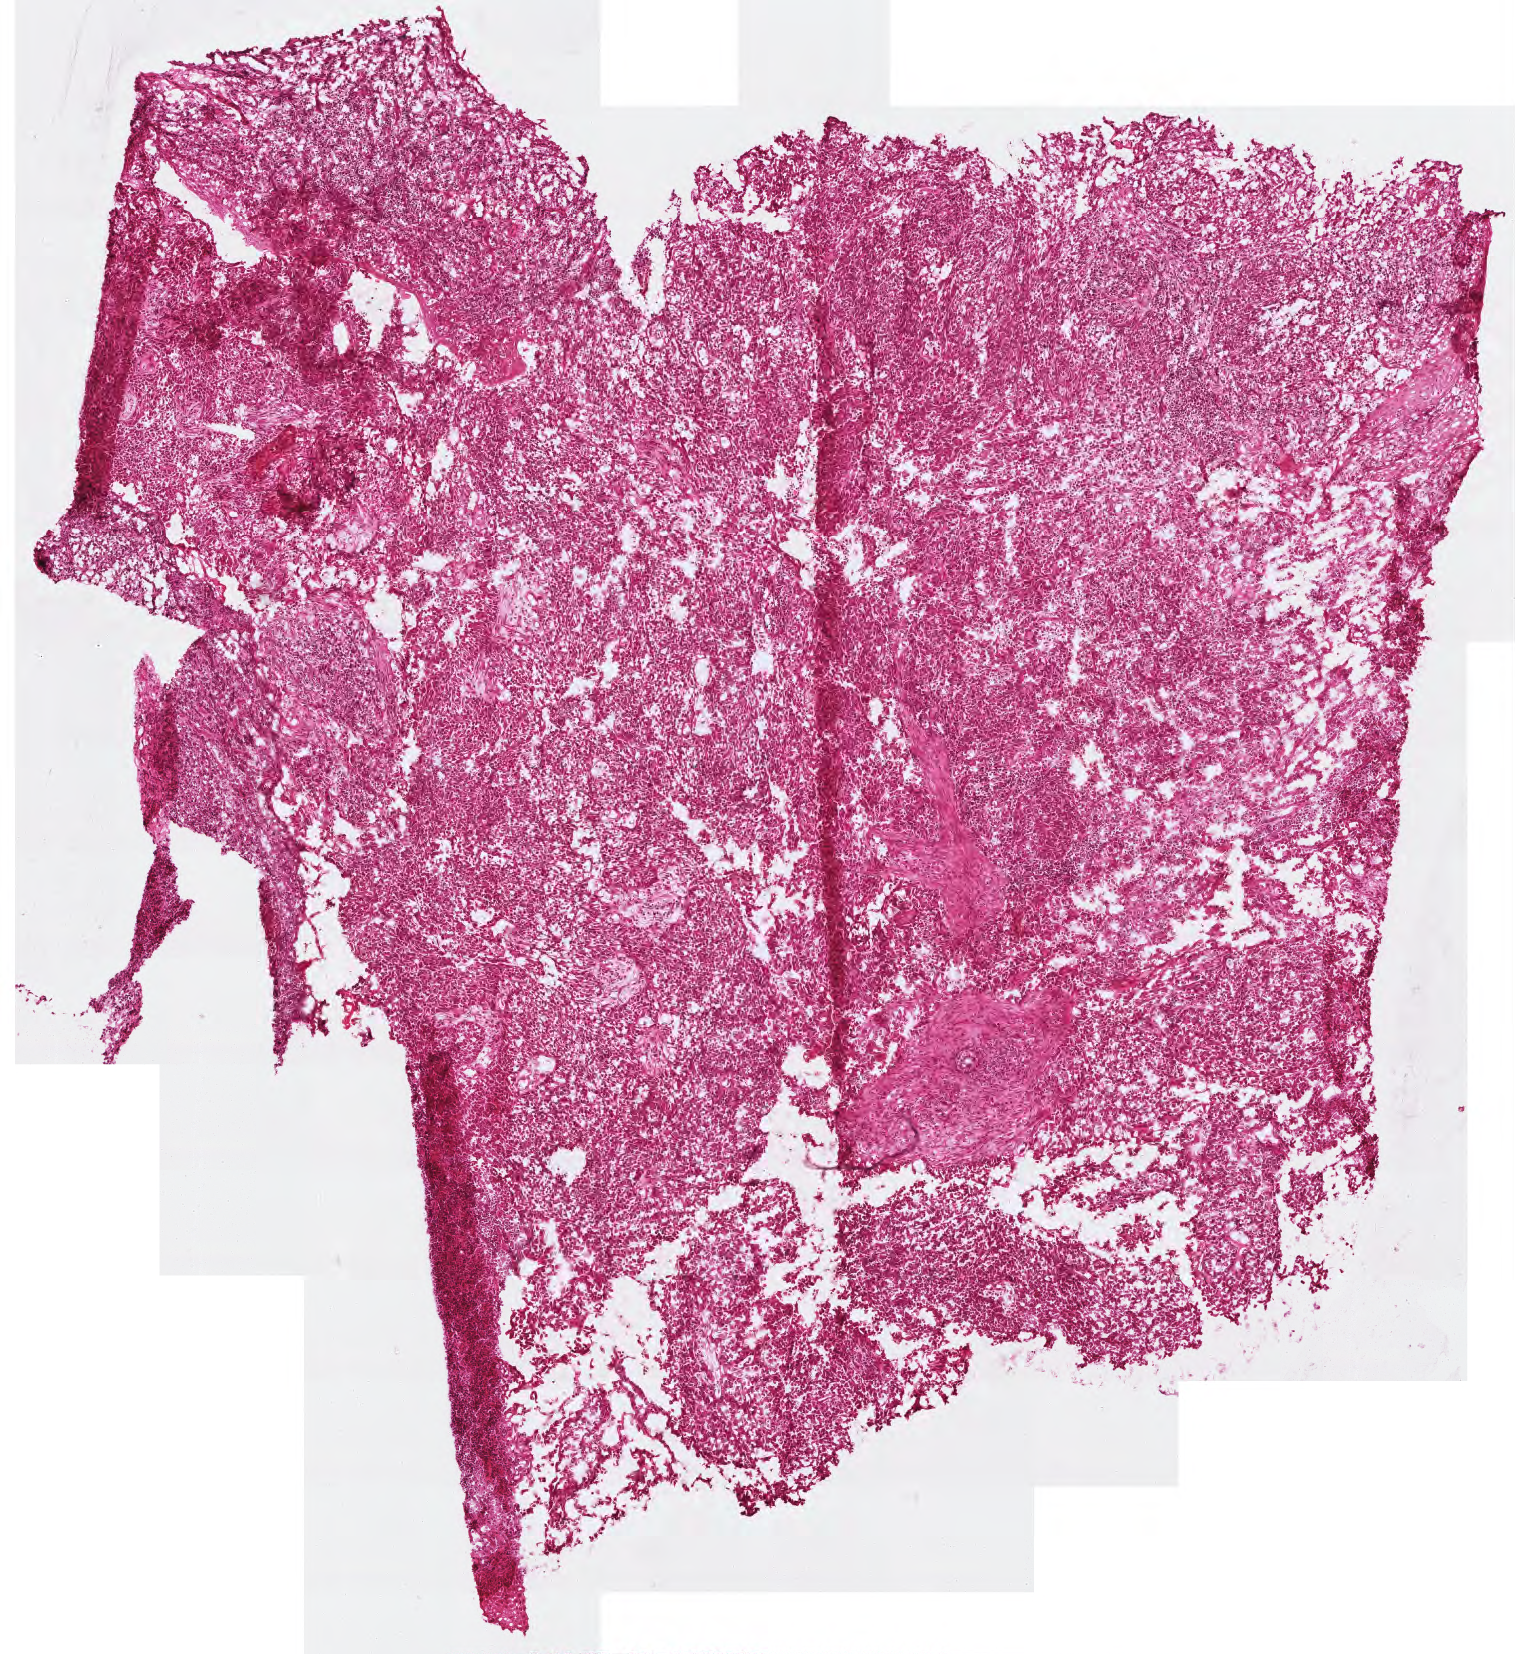
Whole-slide histology image, Hematoxylin and eosin (H&E) stained — whole scanned area (about 3.0 x 3.3 mm) shown as a low-resolution overview. Frozen section from the top of the tissue portion. Primary tumour sample from the head and neck. Patient: male, age at initial diagnosis 62 years. Histologic grade: G3 (poorly differentiated). Pathologist review of this section (percent, as recorded): tumour cells 95%, tumour nuclei 90%, normal cells 0%, stromal cells 5%, necrosis 0%.
• laterality: left
• diagnosis: Squamous cell carcinoma, NOS (tonsil, NOS)